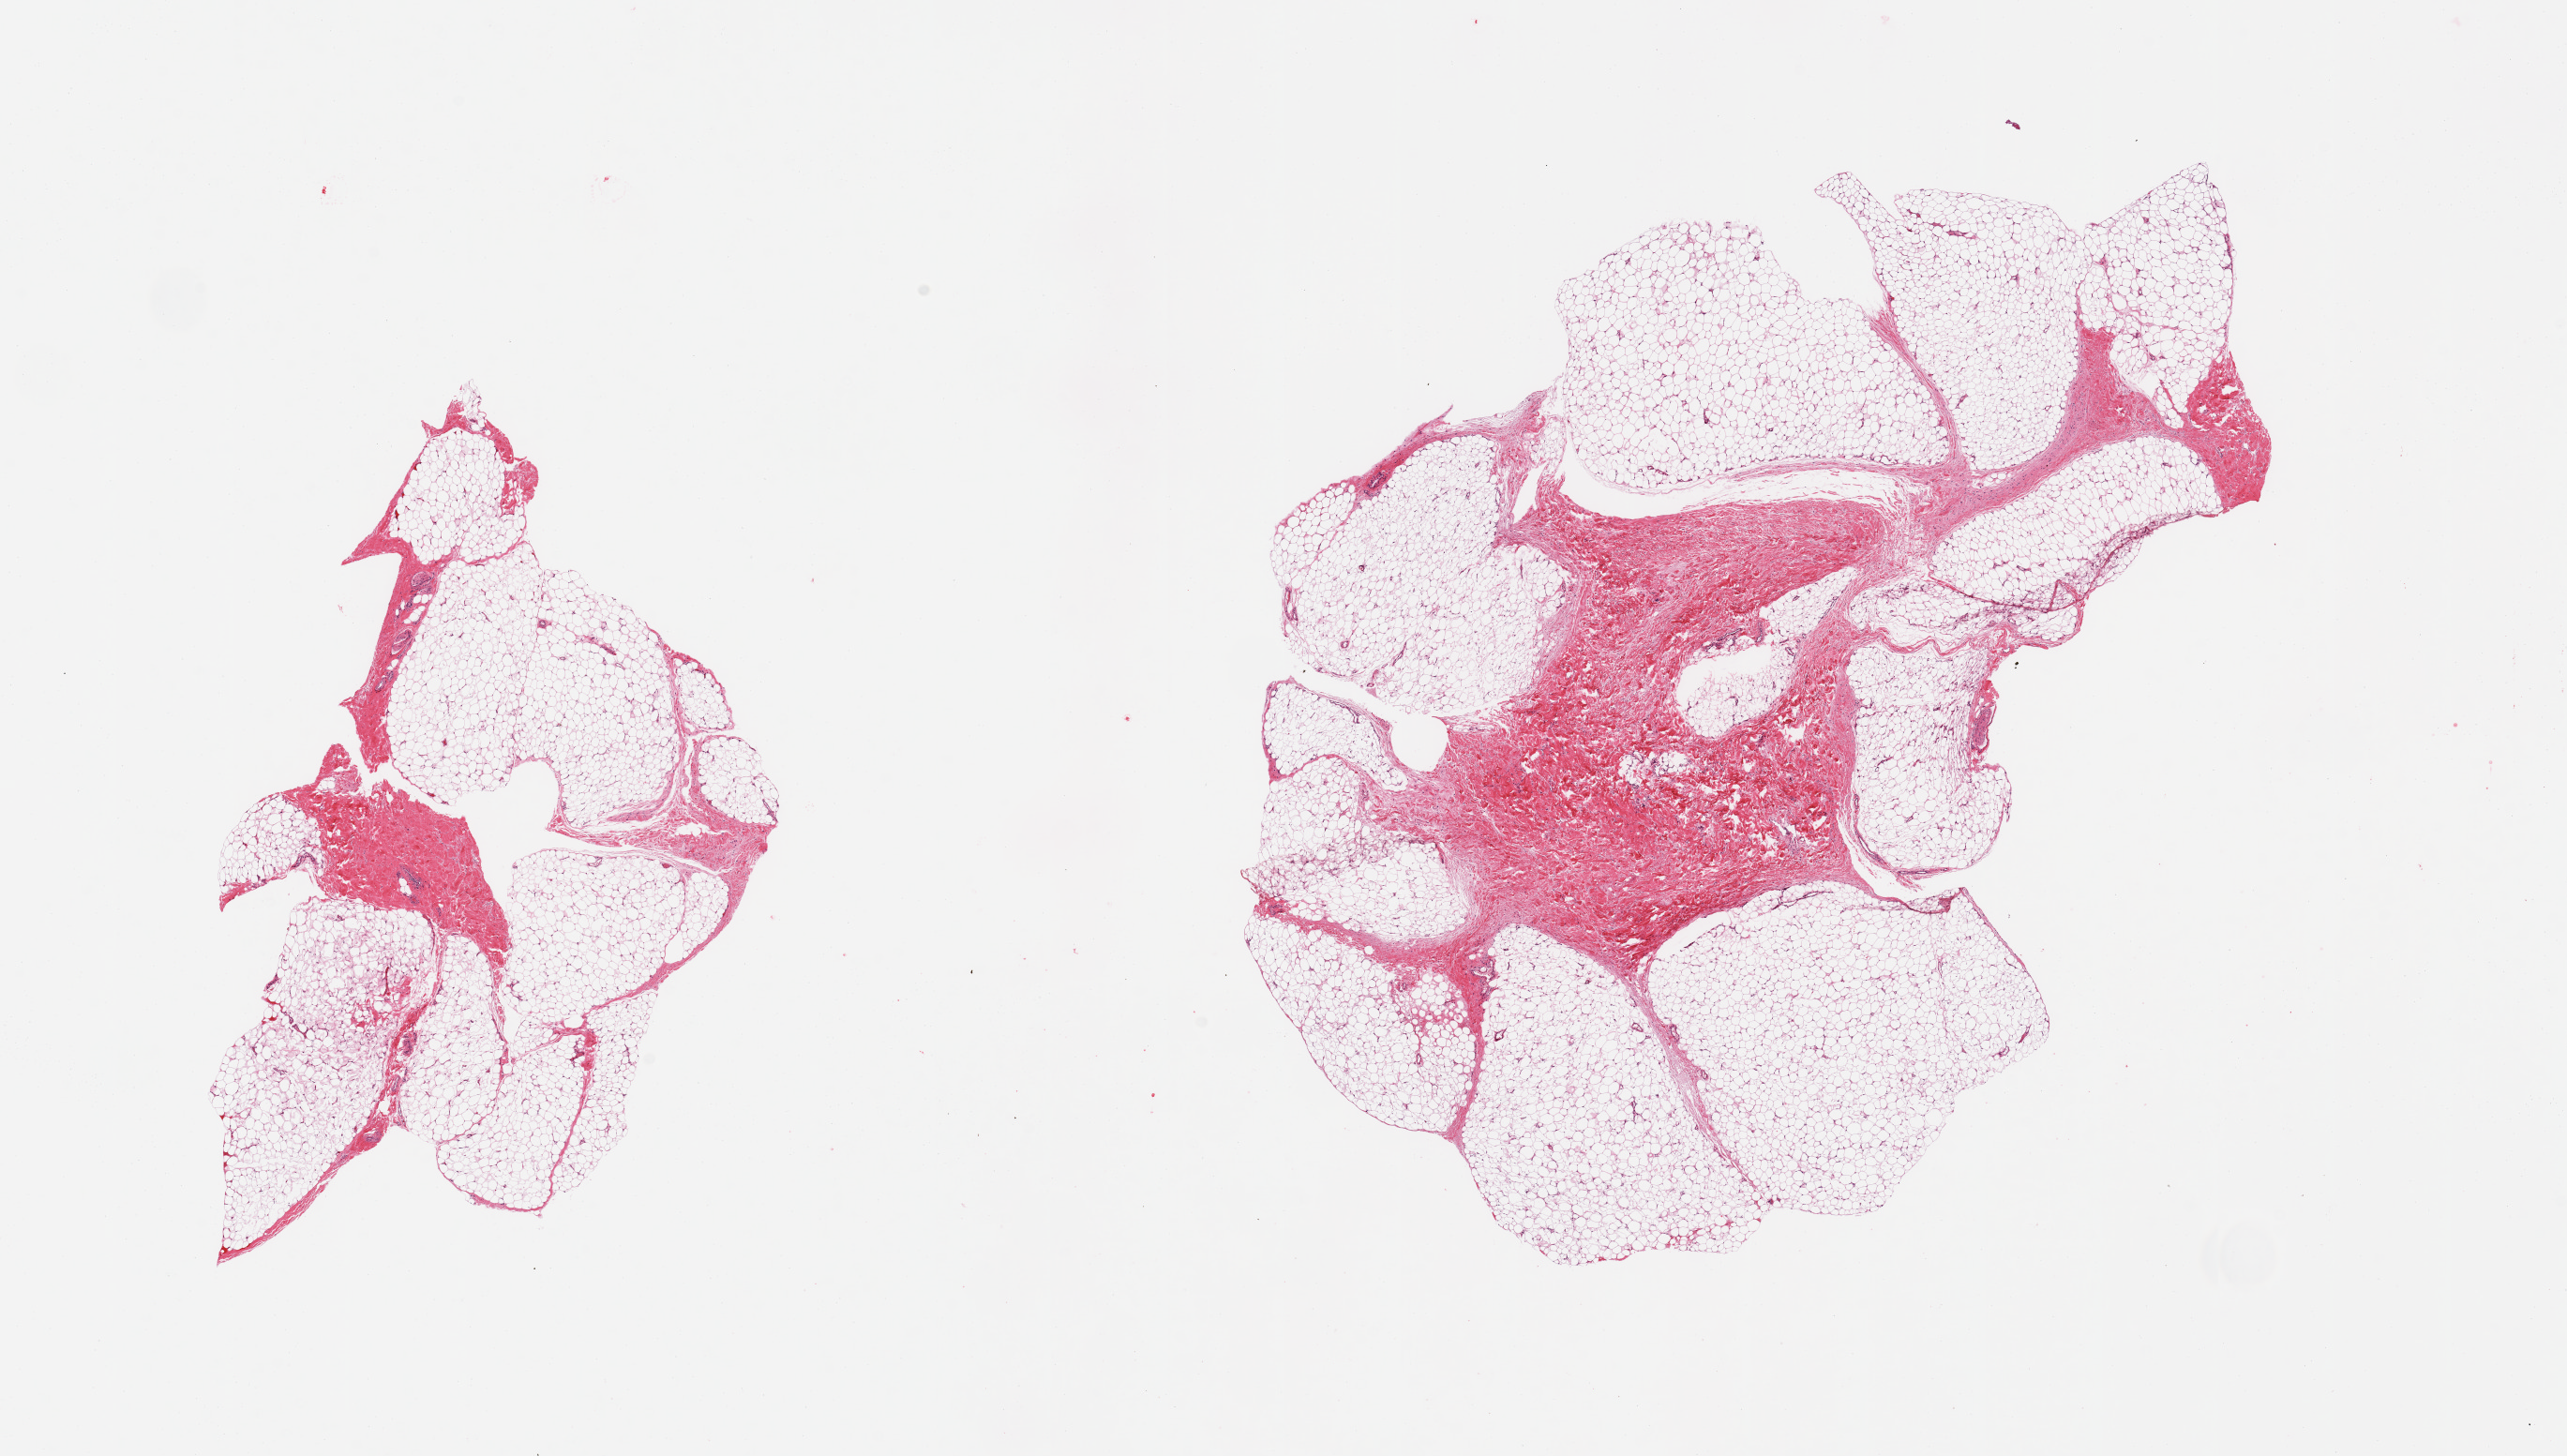
H&E whole-slide image — a low-resolution overview of the entire scanned area, about 21.7 x 12.3 mm (slide scanned at 20x), PAXgene-fixed paraffin-embedded (PFPE) section, target tissue: adipose tissue, tissue donor sample. Donor: male.
Review note (as recorded): 2 pieces, ~30% fascia.